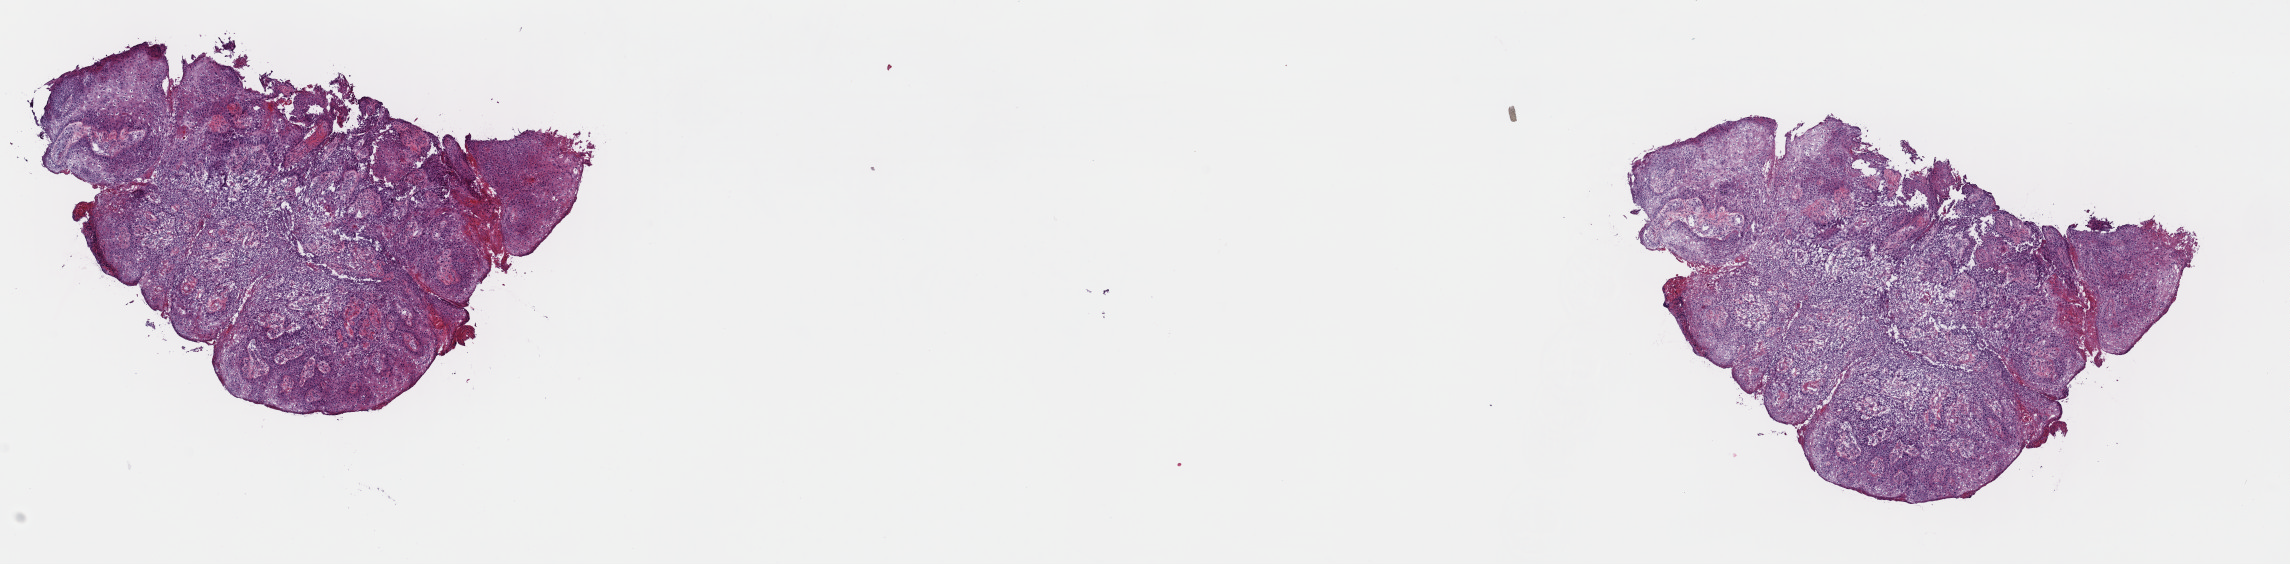
Whole-slide histology image, Hematoxylin and eosin (H&E) stained — whole scanned area (about 18.1 x 4.5 mm) shown as a low-resolution overview, frozen section, sample: primary tumour, head and neck. Female, age 60 years at initial diagnosis. Histologic grade: G2 (moderately differentiated). Slide review estimates, as recorded: tumour cells 90%, tumour nuclei 90%, normal cells 0%, stromal cells 10%, necrosis 0%. Infiltration values recorded for this section: lymphocyte infiltration 5%, monocyte infiltration 0%, neutrophil infiltration 0%.
Pathologic diagnosis: Squamous cell carcinoma, large cell, nonkeratinizing, NOS. AJCC pathologic stage: II (7th edition).